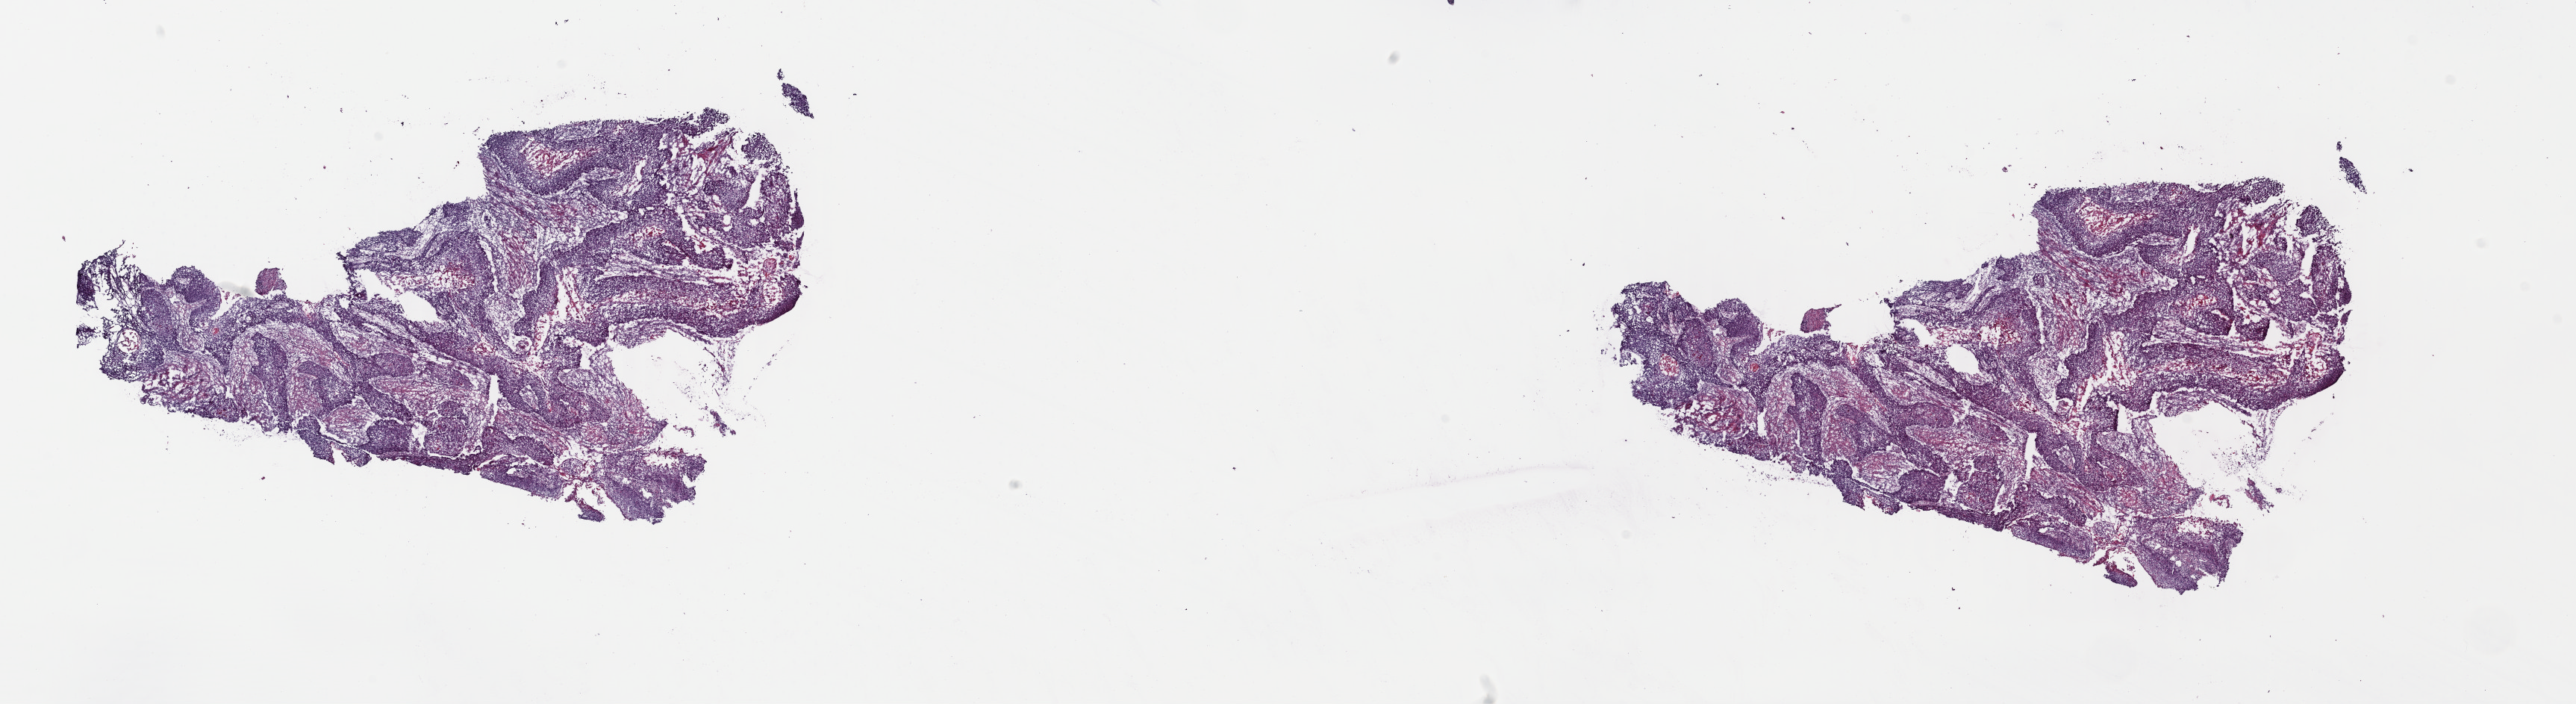
Digitized Hematoxylin and eosin (H&E) stained tissue section (whole slide) — a low-resolution overview of the entire scanned area, about 27.1 x 7.4 mm (from a 40x scan); frozen section from the top of the tissue portion; sample: primary tumour, esophagus. Male, age 57 years at initial diagnosis. Histologic grade: G2 (moderately differentiated). Pathologist review of this section (percent, as recorded): tumour cells 100%, tumour nuclei 80%, normal cells 0%, stromal cells 0%, necrosis 0%. Infiltration values recorded for this section: lymphocyte infiltration 3%, monocyte infiltration 0%, neutrophil infiltration 0%.
AJCC pathologic stage: IIA (6th edition). TNM: T2 N0 M0. Diagnosis: Squamous cell carcinoma, NOS.